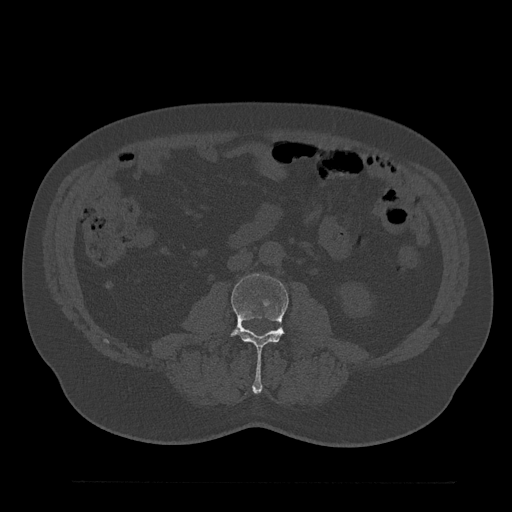
CT including the spine, one axial slice. Slice 29 of 797 in the series (ordered by position). 120 kVp. Bone window (W 1800 / L 400 HU). 0.5 mm slice thickness. 512 × 512 image matrix, field of view 430 × 430 mm. Patient: male, 61 years. Case-level facts recorded for this patient, not image findings: primary cancer: prostate.
Annotated regions visible in this slice (semi-automatic segmentation, software-assisted and operator-edited):
- L3 vertebra: bounding box [x1, y1, x2, y2] px = [229, 274, 289, 394]